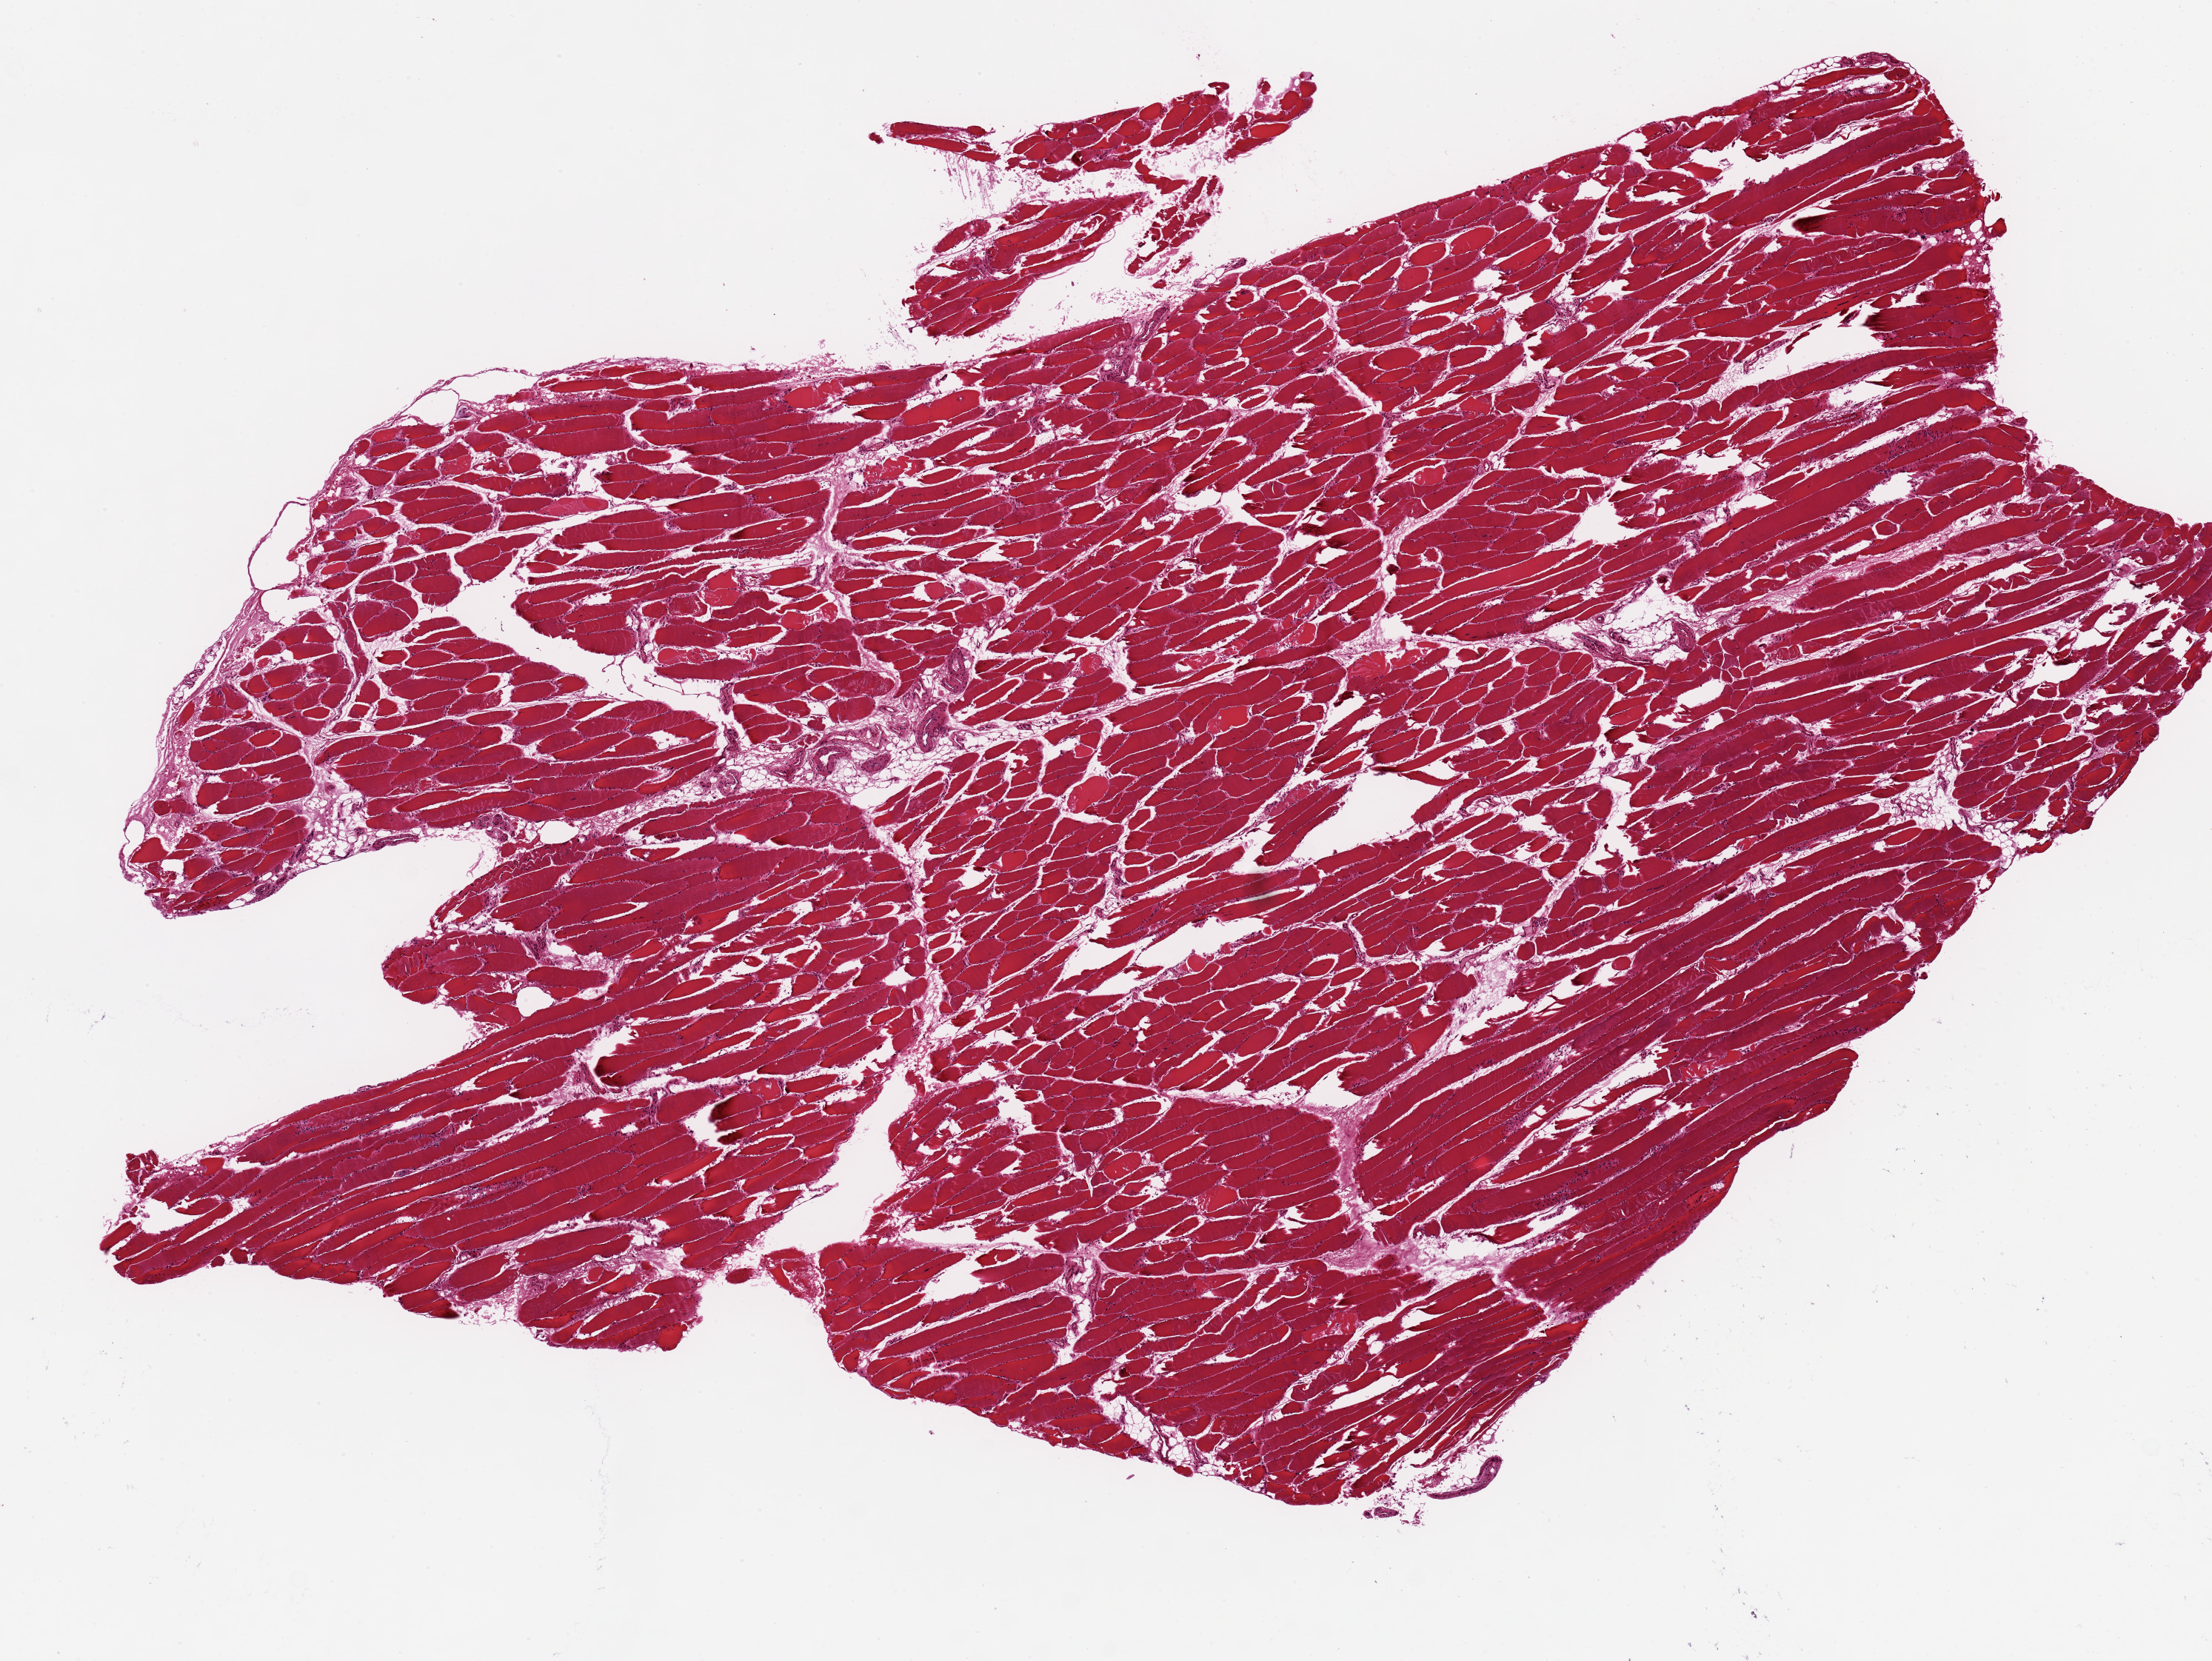
Hematoxylin and eosin (H&E) whole-slide image, whole scanned area (about 11.8 x 8.9 mm, slide scanned at 20x) shown as a low-resolution overview. PAXgene-fixed paraffin-embedded (PFPE) section. Section of stomach (target tissue). Tissue donor sample. Donor: female.
Reviewer comment on this tissue sample: 2 (varies from 1-3).